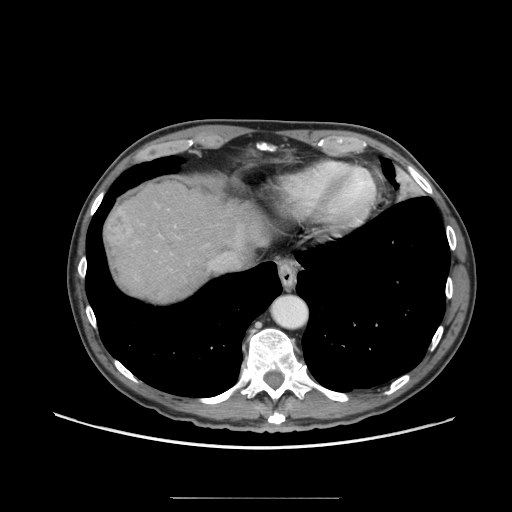
Contrast-enhanced abdominal CT (liver protocol), one axial slice; position 59 of 71 along the scan axis; reconstruction kernel STANDARD; 140 kVp; soft-tissue window (W 400 / L 40 HU); 512 × 512 image matrix, field of view 400 × 400 mm. From the clinical record (not read from this slice): diagnosis: hepatocellular carcinoma (patient treated with transarterial chemoembolisation; whether this scan precedes or follows treatment is not stated here); TNM stage (as recorded): Stage-I; Child-Pugh class: A; tumour nodularity: uninodular.
Structures marked on this image (semi-automatically segmented with operator editing):
- abdominal aorta: bounding box (x1, y1, x2, y2) in pixels: (273, 296, 307, 328)
- liver parenchyma outside the tumour (the mass and vessels are separate outlines, so this box may not span the whole liver): (106, 182, 270, 302)
- mass: (105, 210, 134, 246)
- liver vessels: (217, 254, 226, 262)